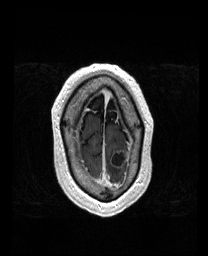
Brain MRI from a brain-tumour surgery series, one axial slice; slice 155 of 192 in the series (ordered by position); T1-weighted post-contrast; 208 × 256 image matrix, field of view 211 × 260 mm. Case-level facts recorded for this patient, not image findings: histopathology: Metastatic Carcinoma from Lung Adenocarcinoma; tumour location: Left Frontal.
Annotated regions visible in this slice (manually delineated by an expert):
- tumour: bounding box (x1, y1, x2, y2) in pixels: (112, 150, 126, 166)